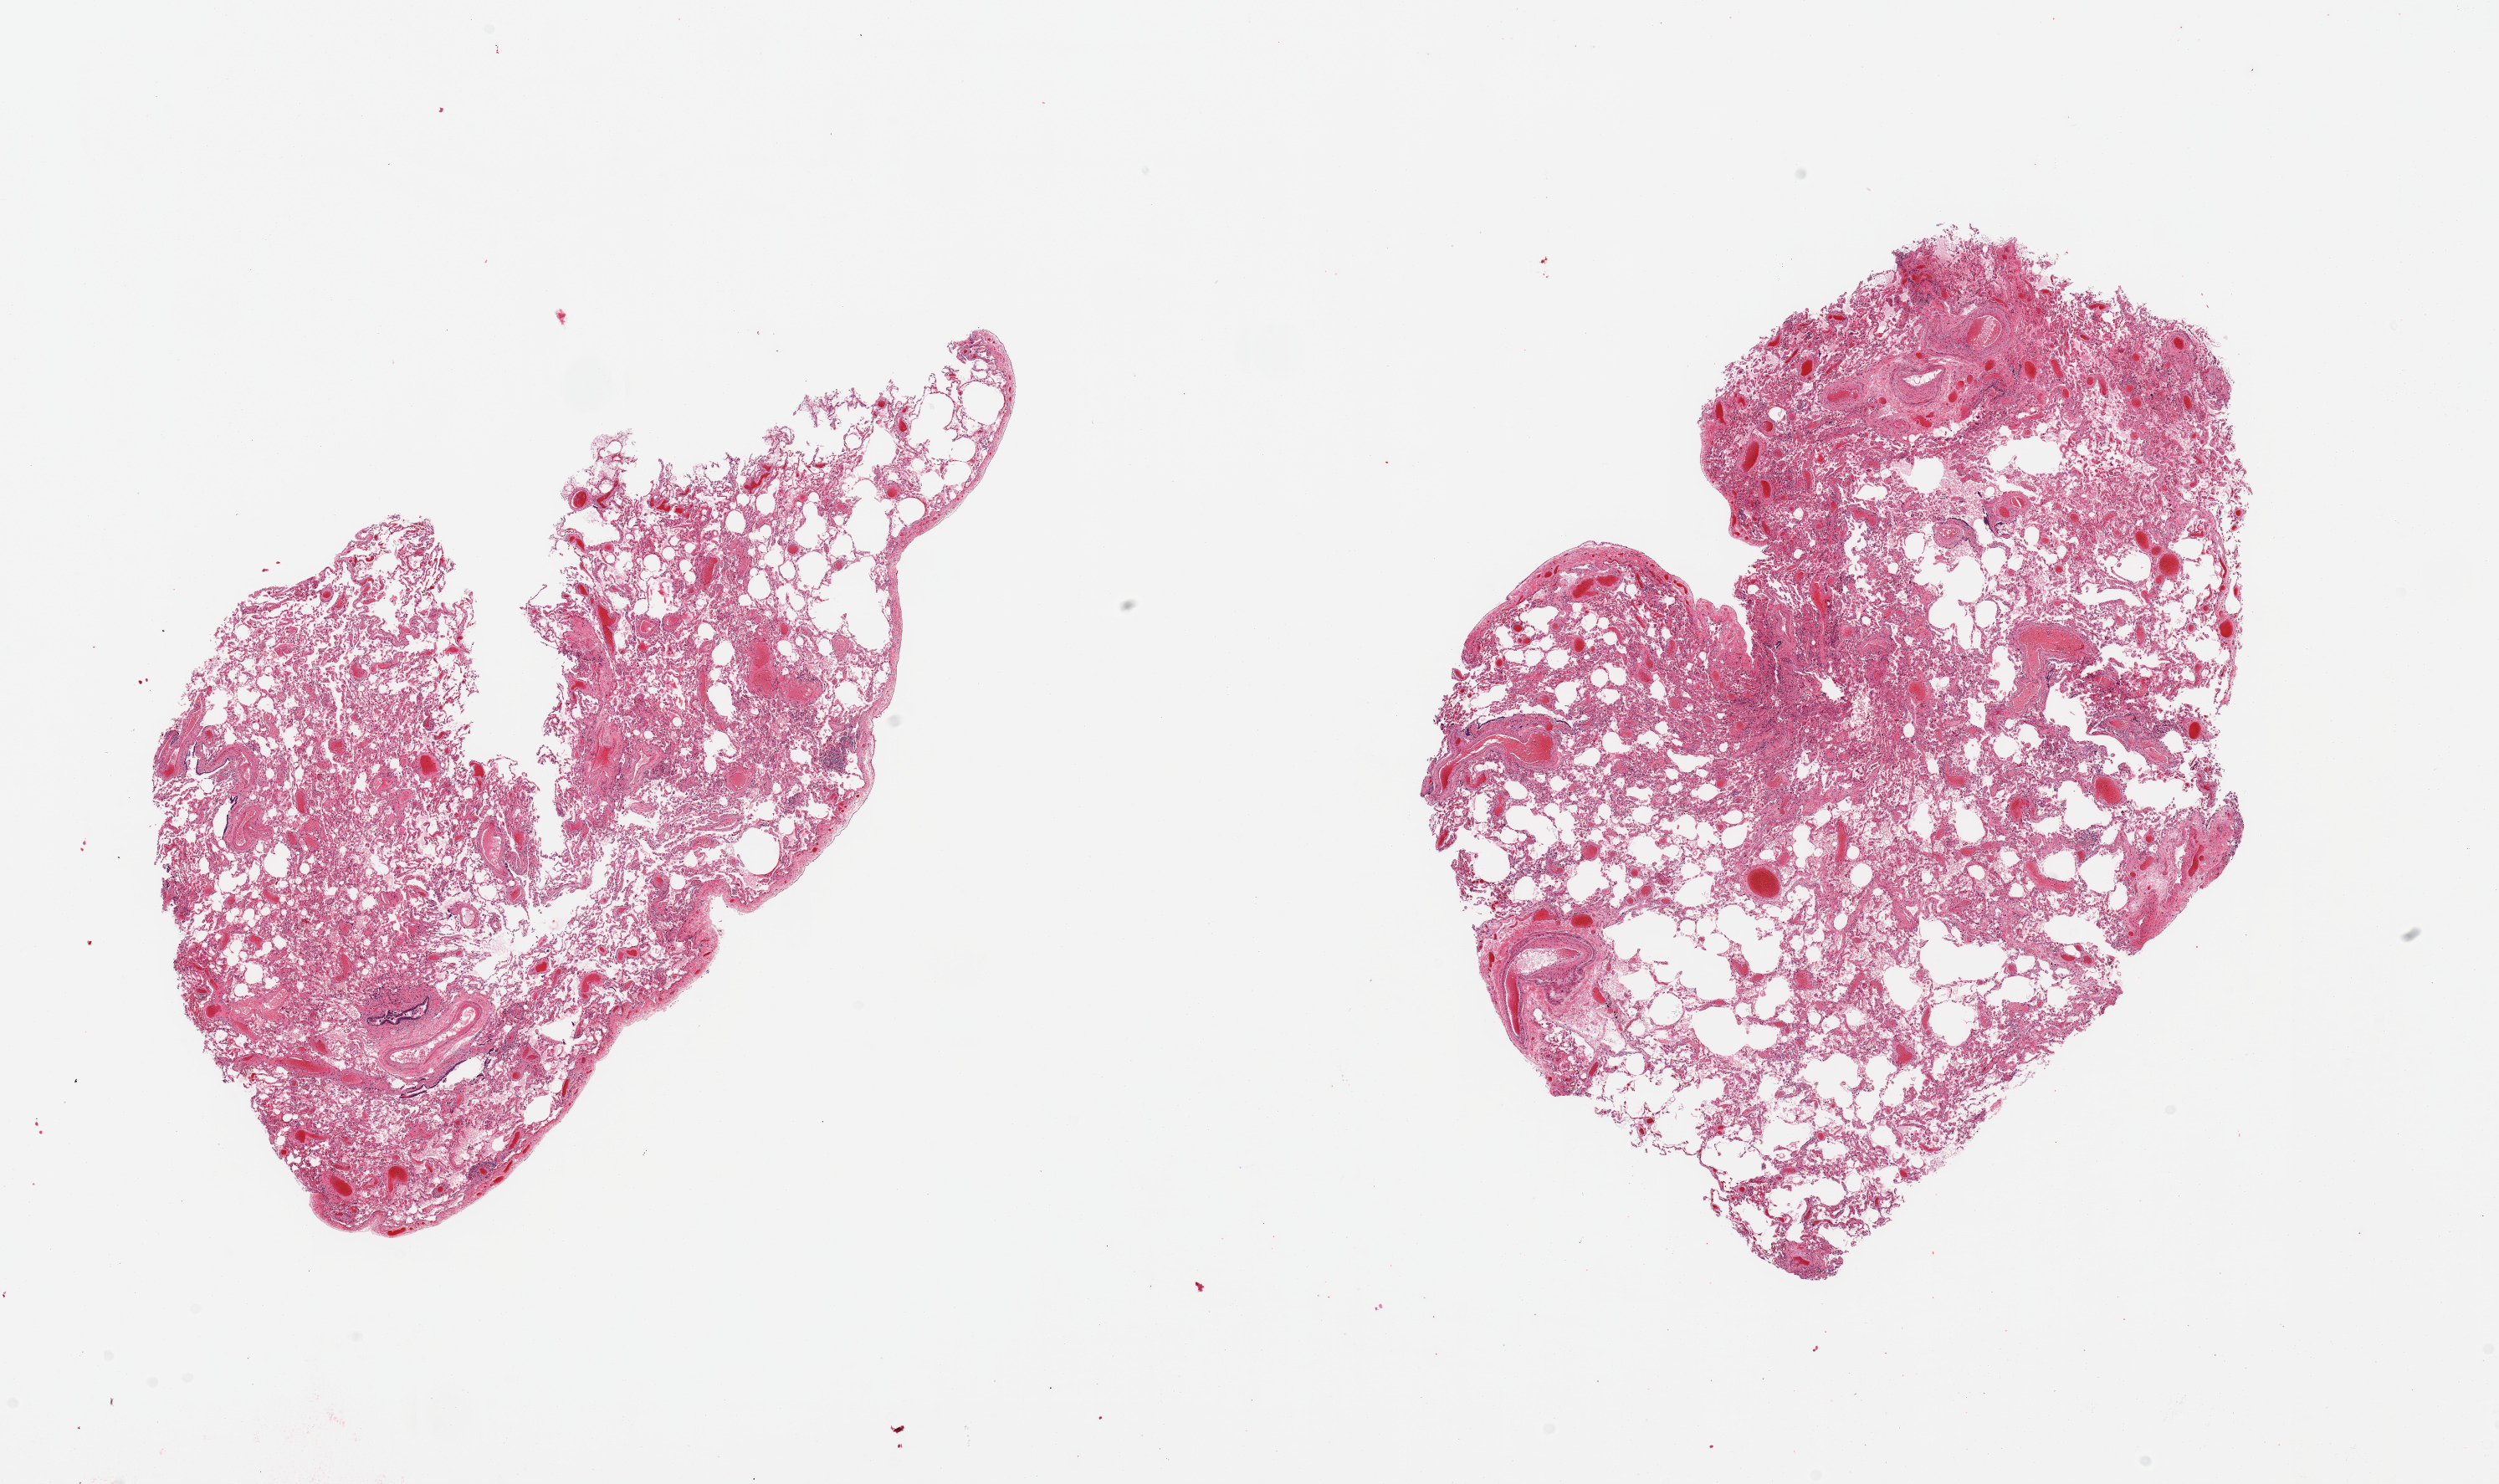
Digitized H&E-stained section — a low-resolution overview of the entire scanned area, about 23.6 x 14.0 mm (slide scanned at 20x), PAXgene-fixed, paraffin-embedded tissue, sampled site (target tissue): lung, donor tissue sample. Male donor.
Reviewer comment on this tissue sample: 2 pieces; moderate vascular congestion and alveolar exudates with patchy emphysema.